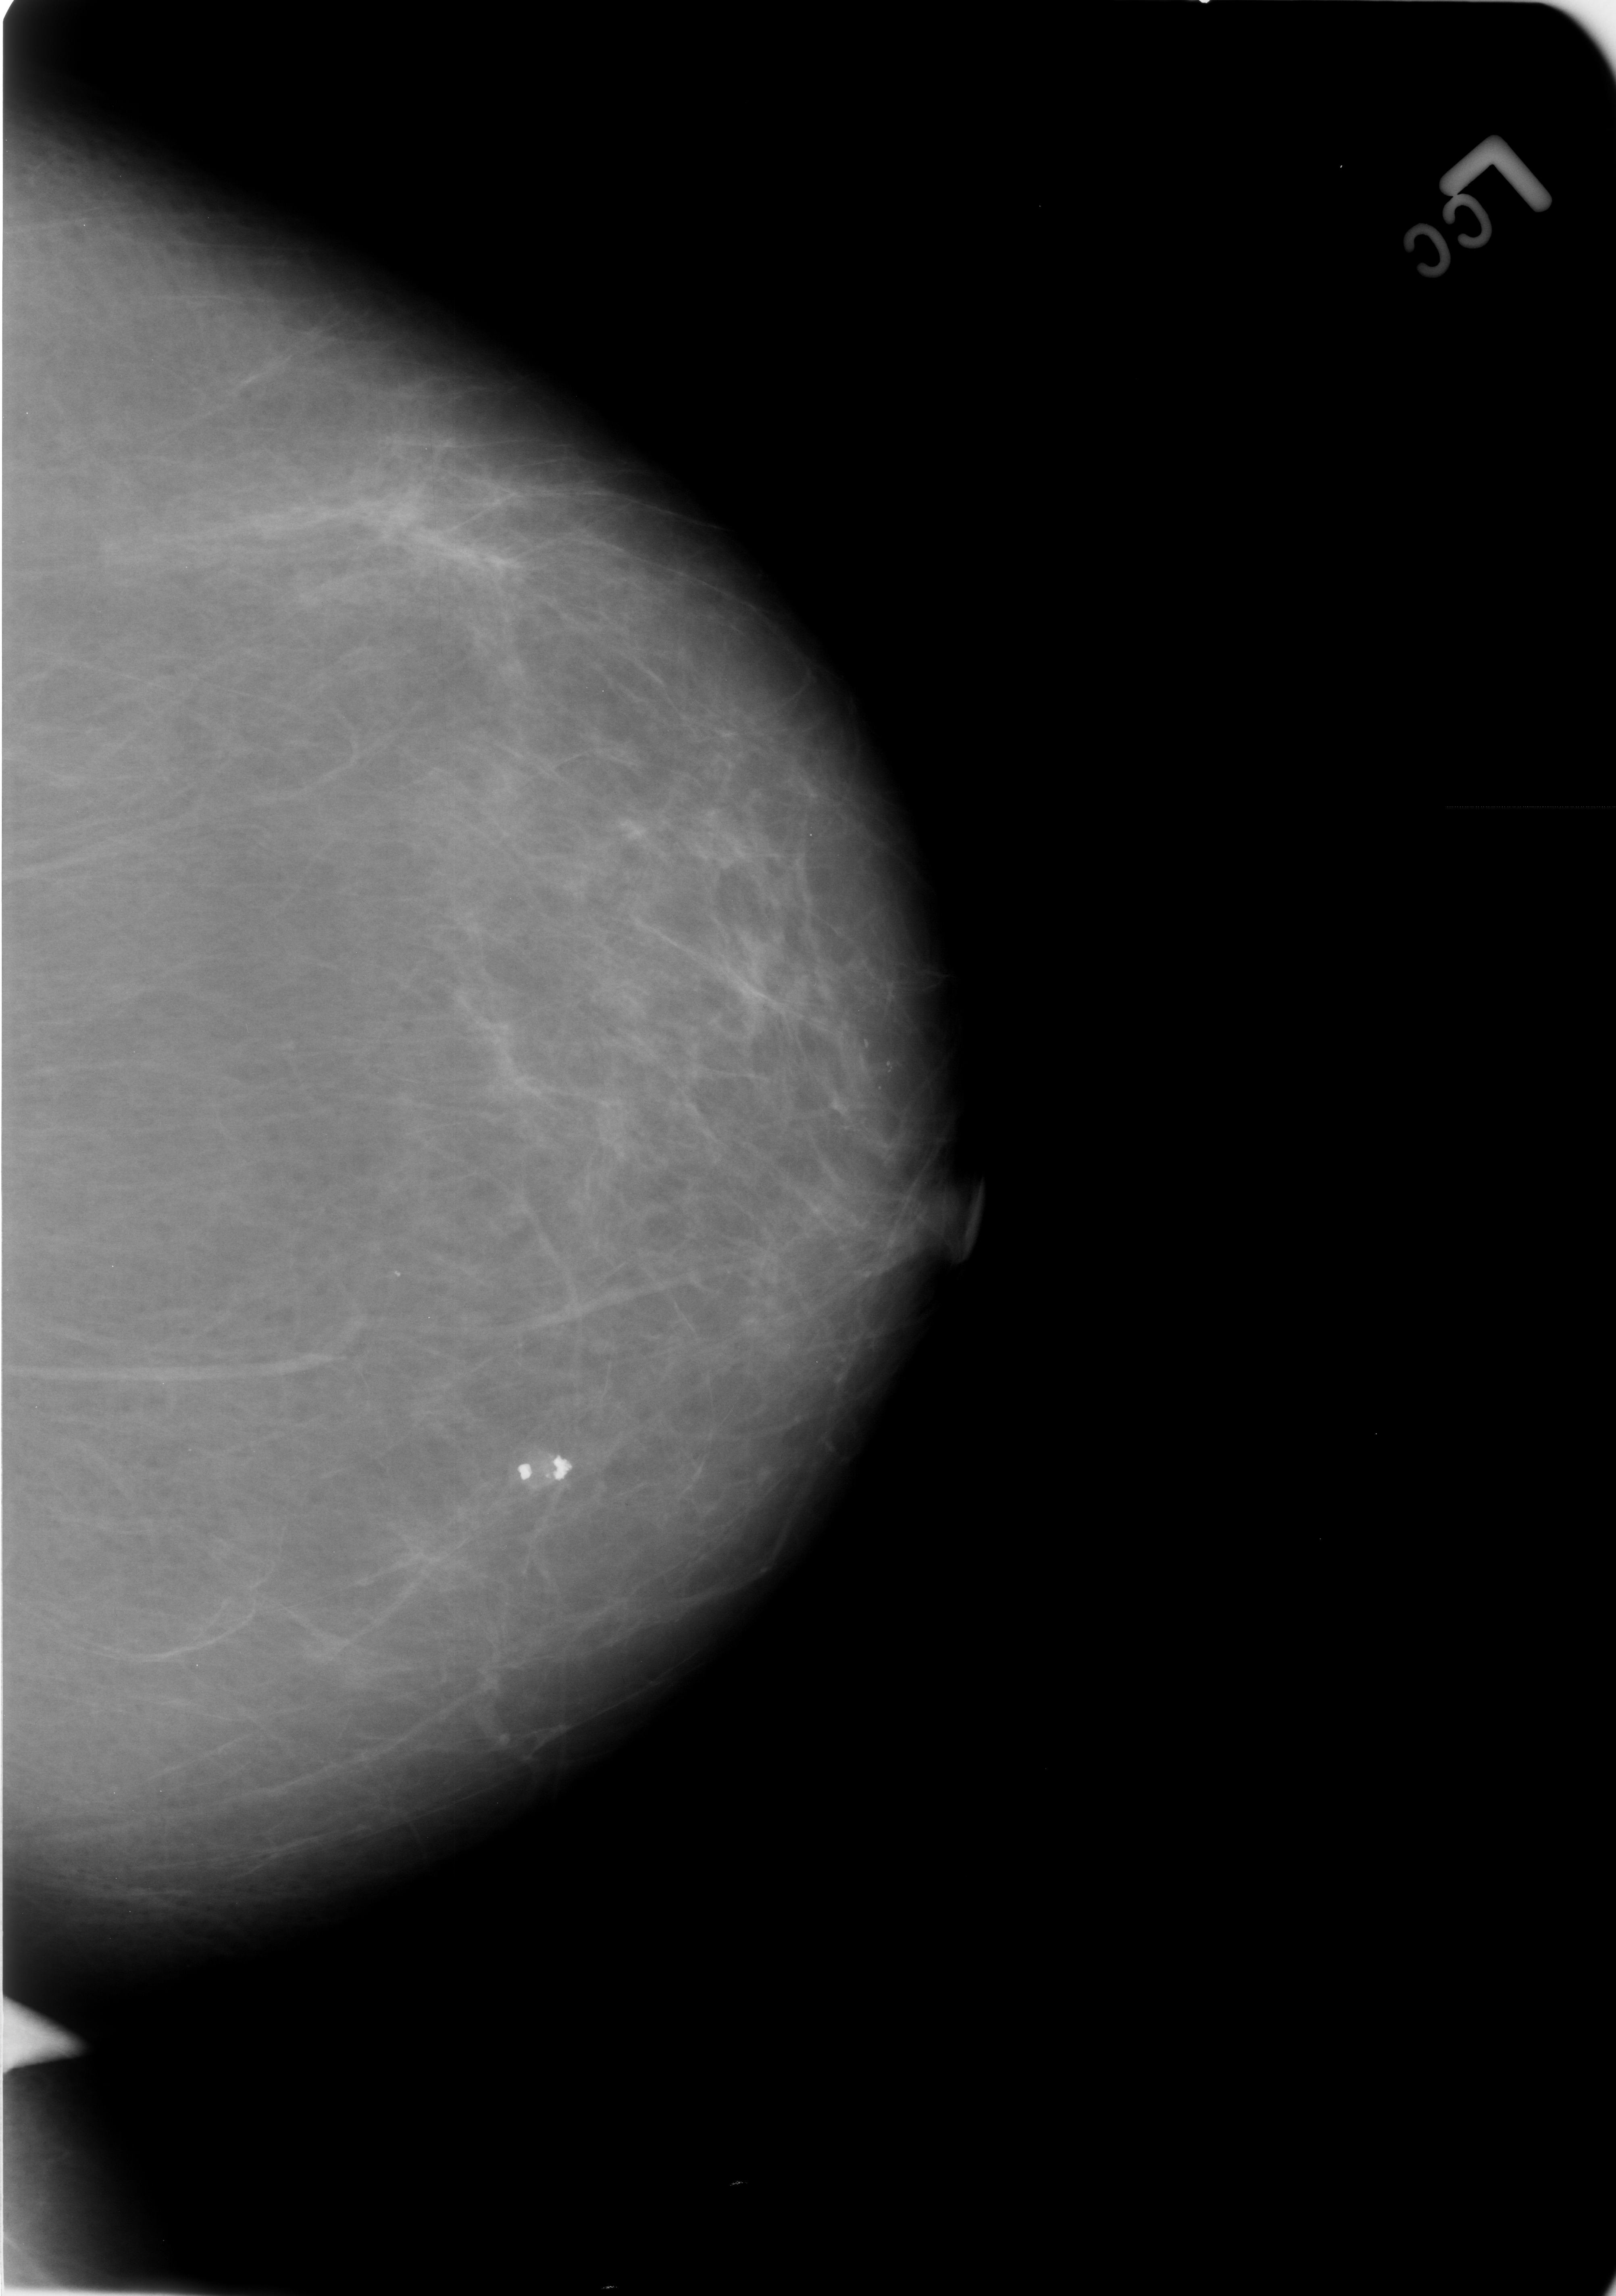
Mammogram (digitized film); left breast; craniocaudal (CC) view; 1616 × 2296 image matrix.
Expert-marked regions of interest on this film, with their recorded descriptors:
- calcifications, morphology coarse; BI-RADS assessment category 2; benign; no additional work-up was recommended (outcome (as recorded, no biopsy): benign without callback): bounding box <499,1454,575,1497> (left, top, right, bottom; pixels)